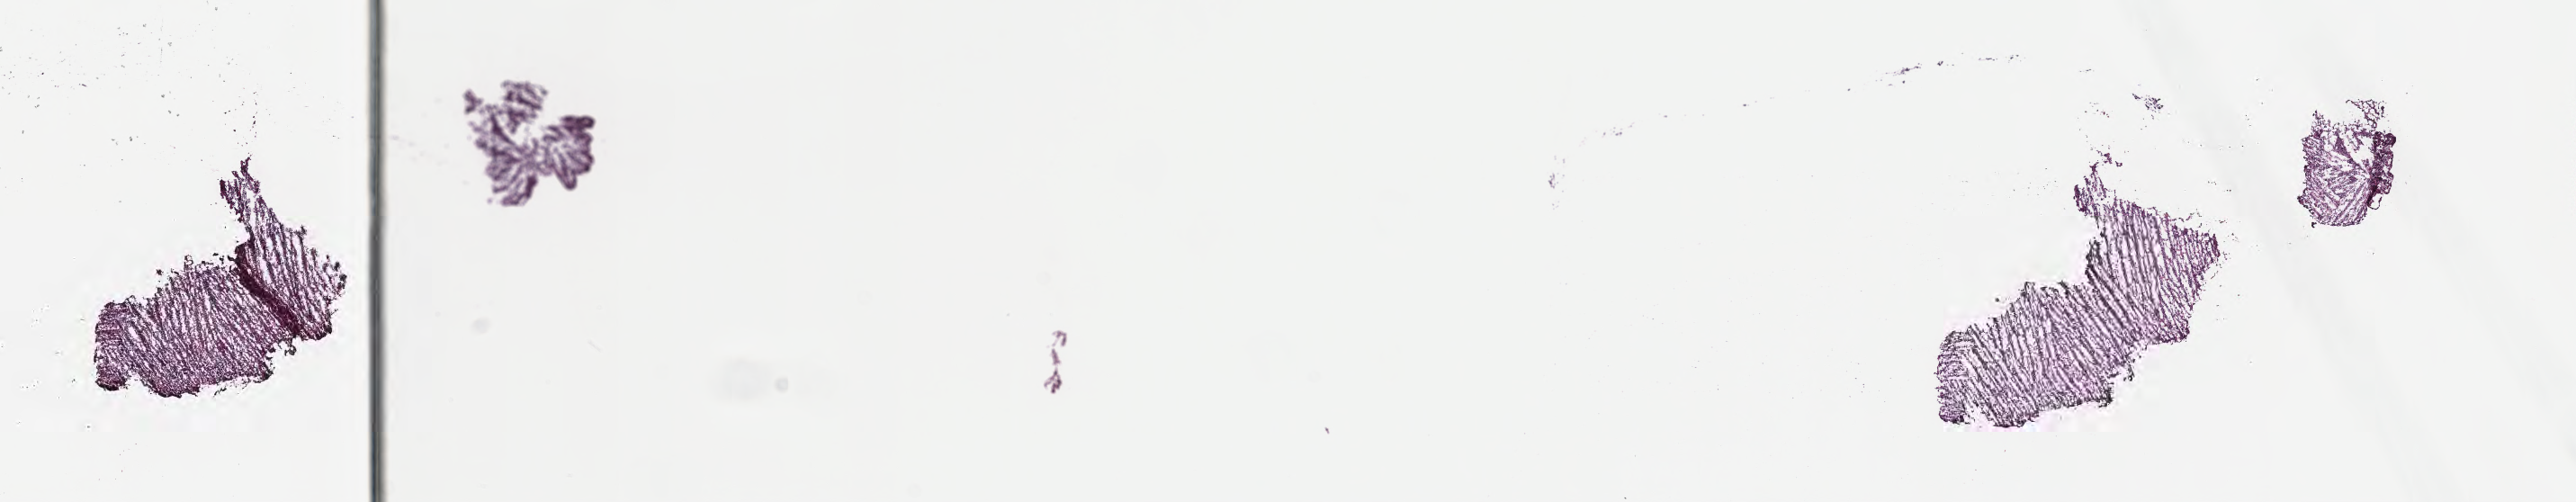
Hematoxylin and eosin (H&E) whole-slide image of tumor tissue from the cerebellum — whole scanned area (about 23.2 x 4.5 mm) shown as a low-resolution overview, cryosection (OCT / tissue freezing medium). Male patient, age 213 months (17 years 9 months).
Recorded diagnosis: Medulloblastoma, NOS.